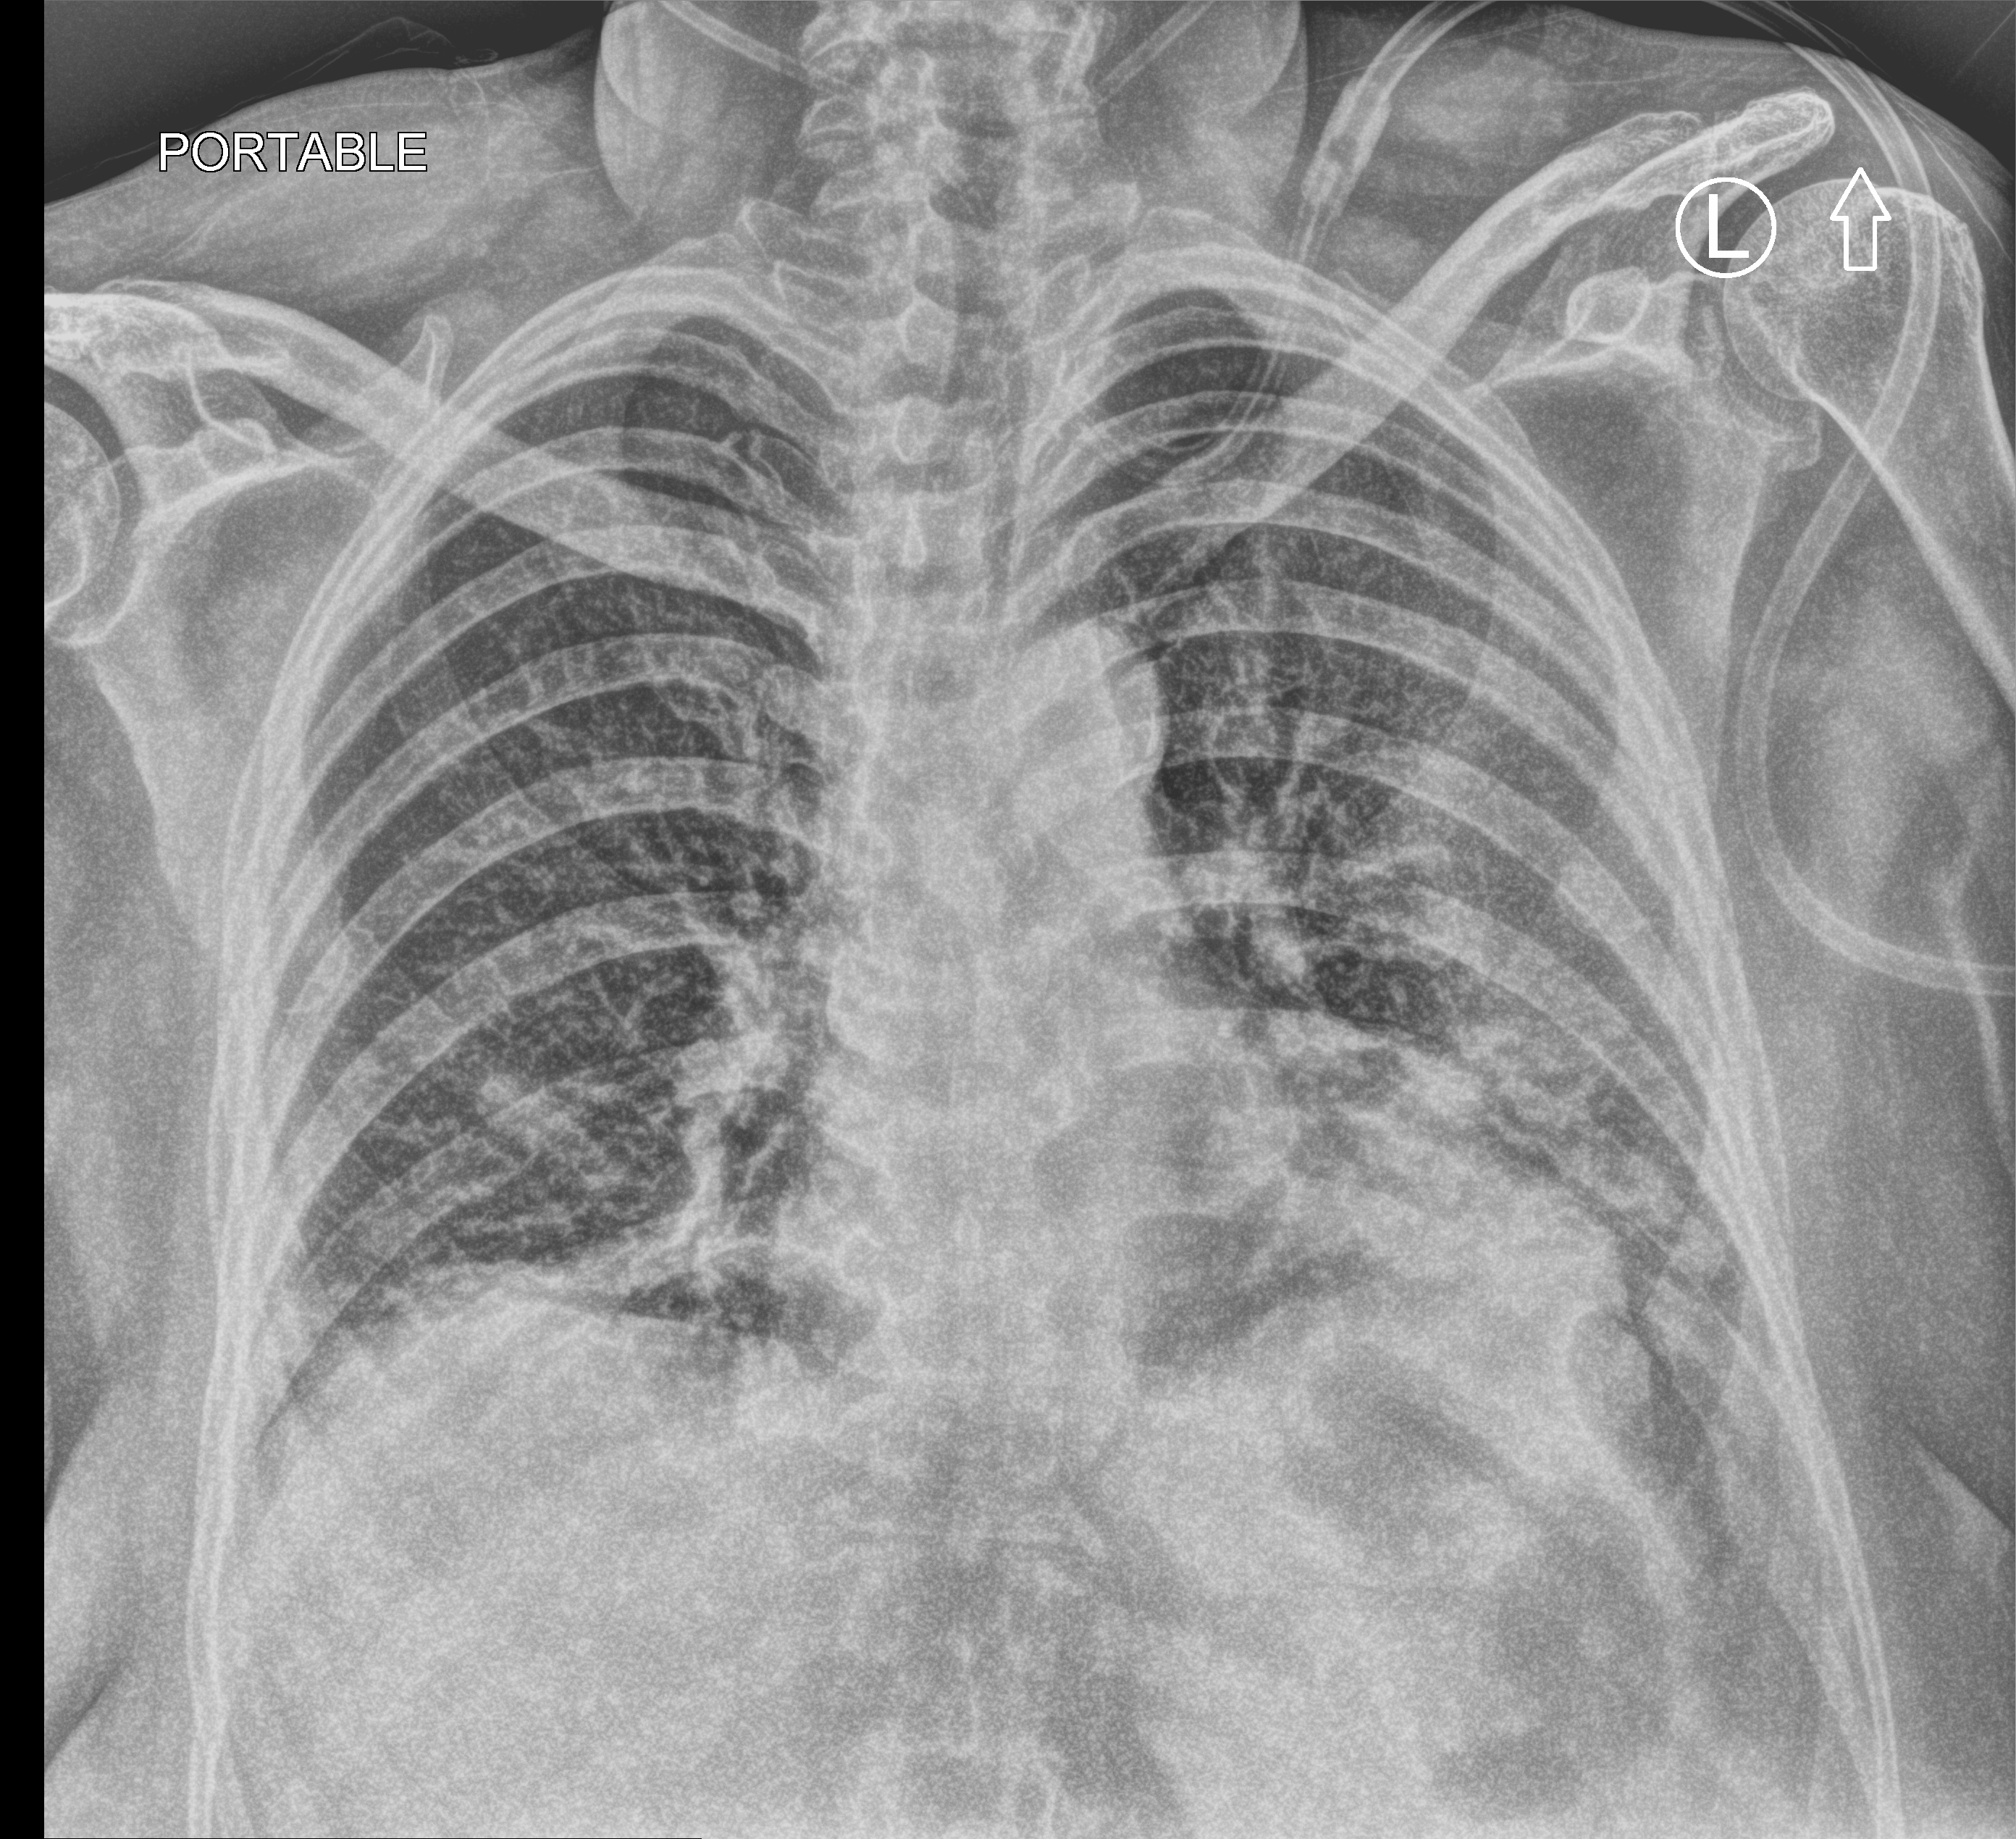
Chest X-ray (portable), anteroposterior (AP) projection. Female patient hospitalised with COVID-19, age 60–74 years.
Hospital-stay facts (about this admission, not read from this image; timing relative to this image not recorded):
- length of hospital stay: 18 days
- mechanically ventilated during this hospital stay: no
- admitted to intensive care during this hospital stay: no